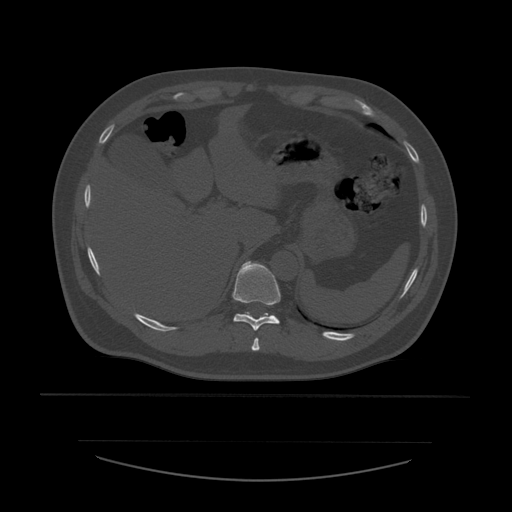
CT including the spine, one axial slice; slice 294 of 532 in the series (ordered by position); bone window (W 1800 / L 400 HU); 1.25 mm slice thickness; 512 × 512 image matrix. Patient age 44 years. Case-level facts recorded for this patient, not image findings: primary cancer: soft tissue sarcoma.
Outlined on this slice (semi-automatic segmentation, software-assisted and operator-edited):
- T10 vertebra: bounding box (x1, y1, x2, y2) in pixels: (233, 262, 281, 331)
- T9 vertebra: (252, 338, 260, 351)